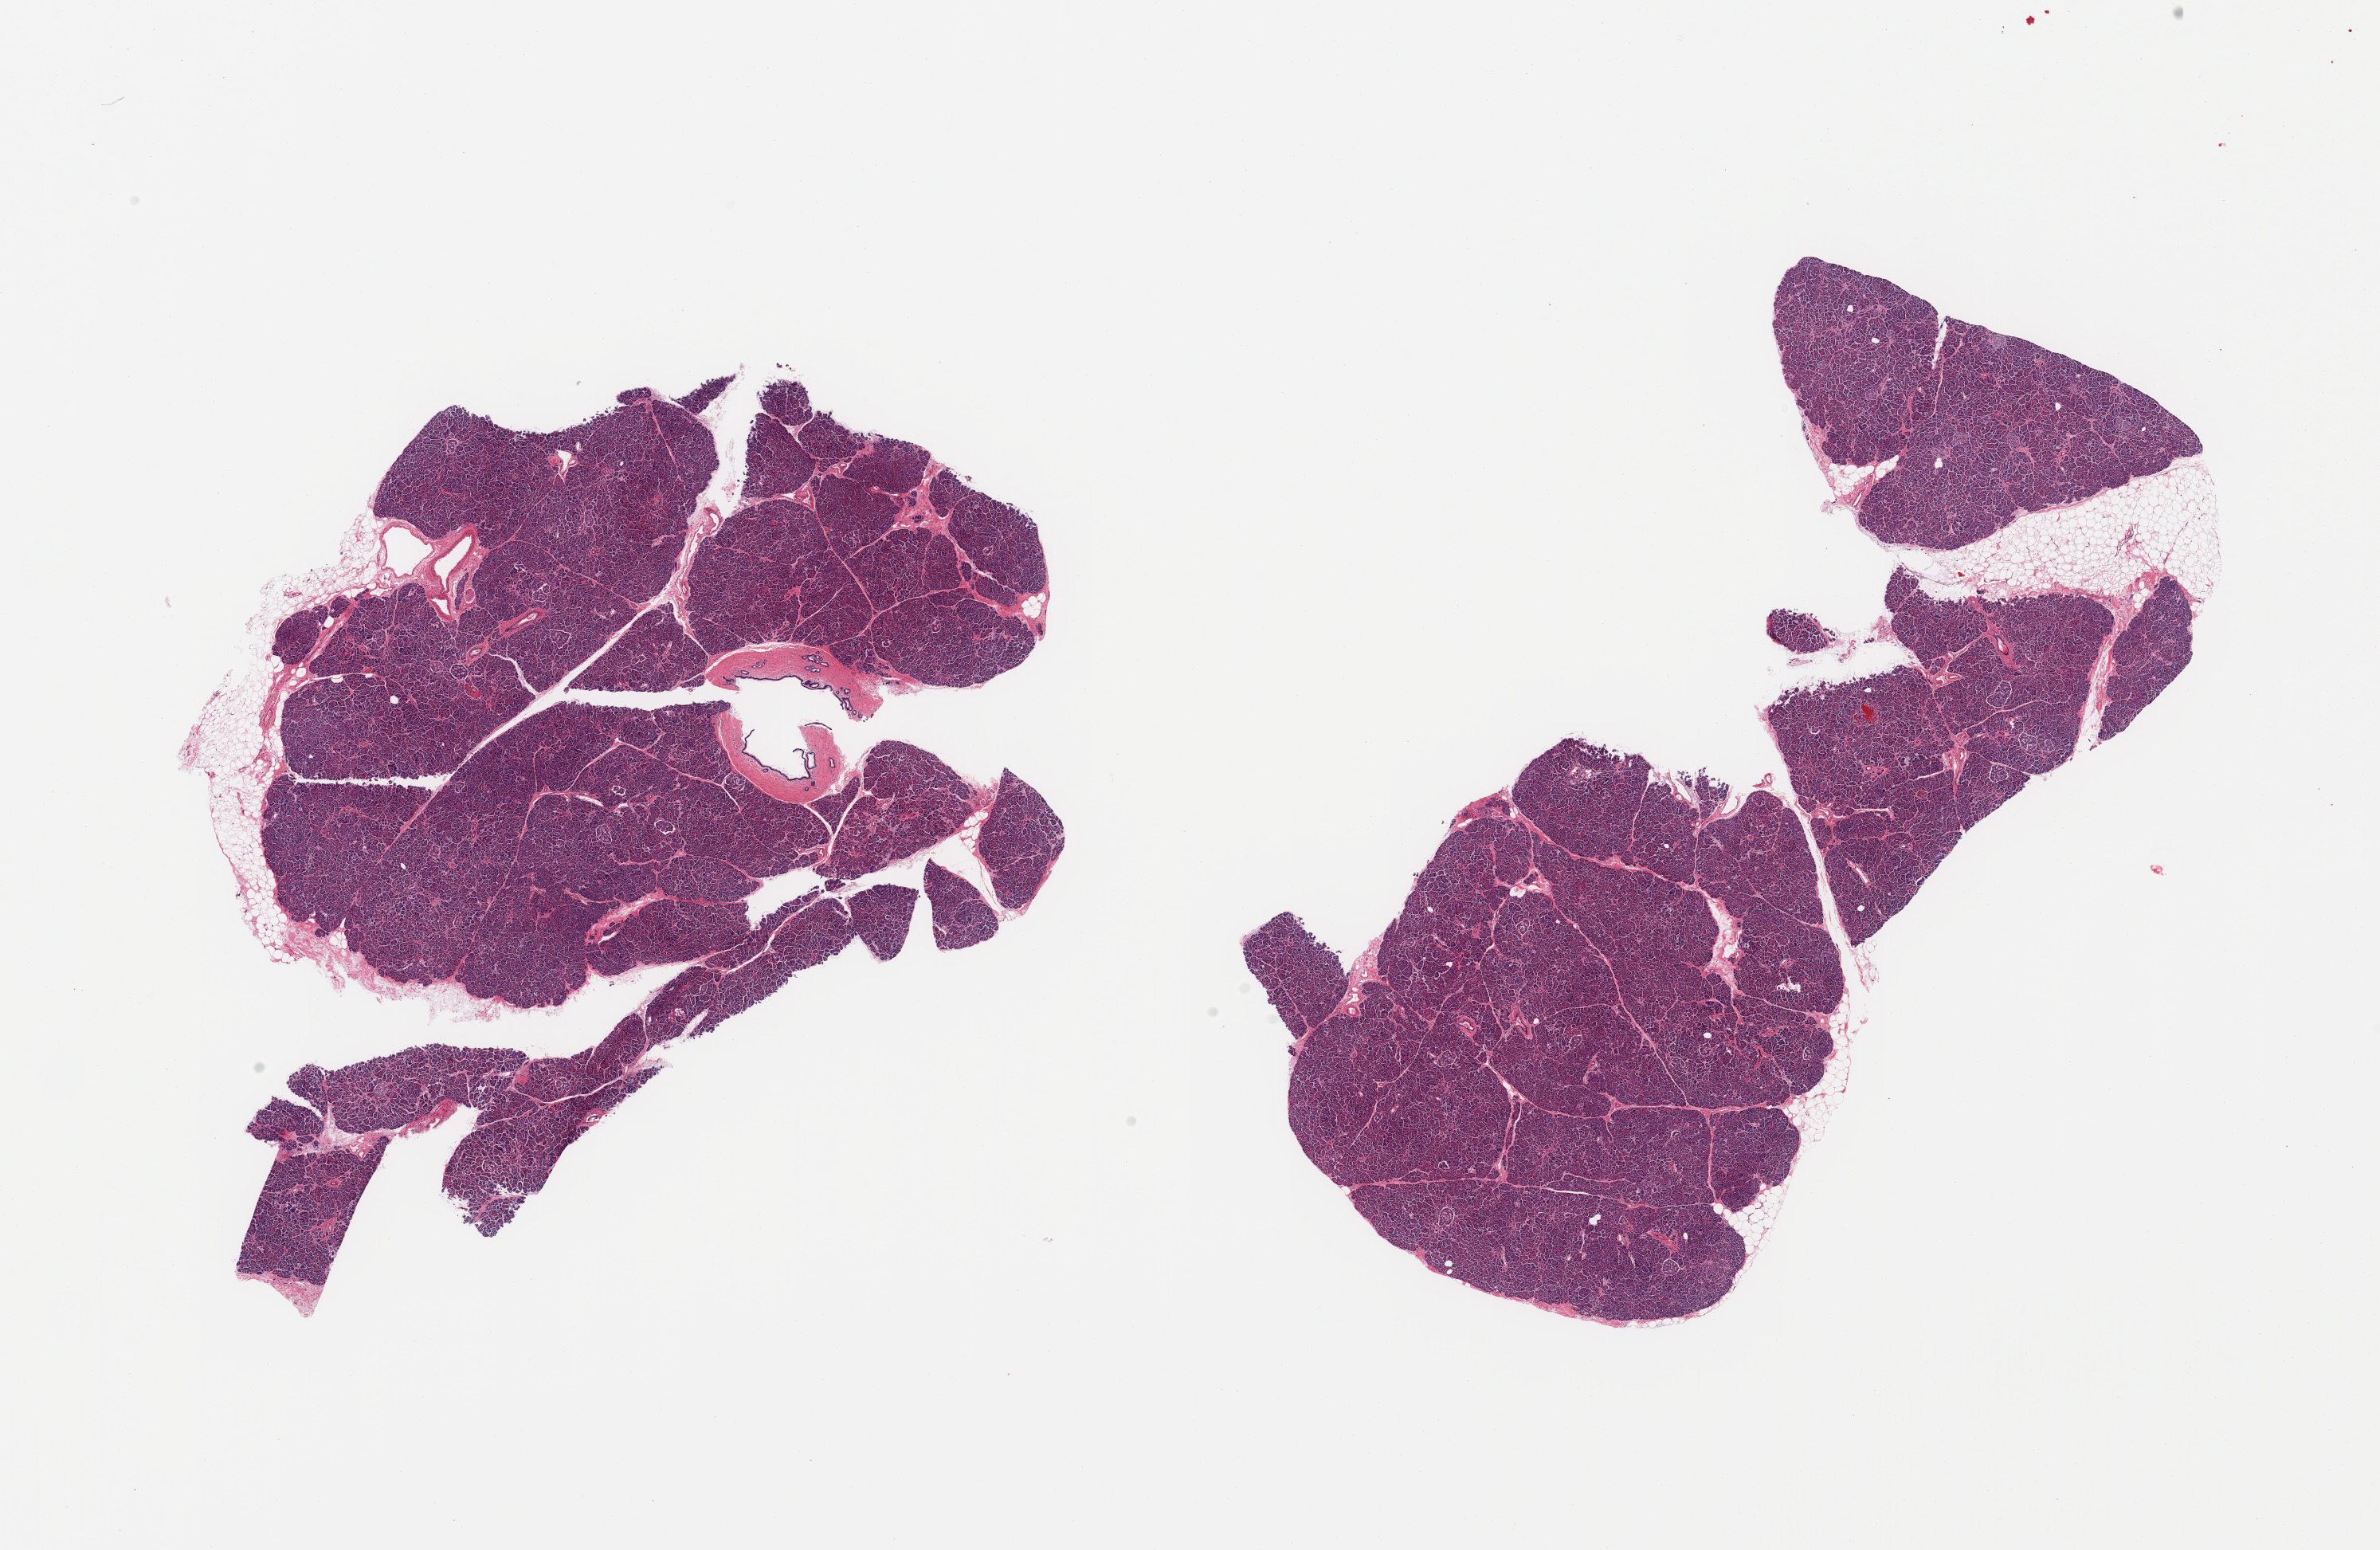
Whole-slide image, haematoxylin and eosin stain, brightfield, shown as a low-resolution overview of the whole scanned area (about 23.6 x 15.4 mm), PAXgene-fixed paraffin-embedded (PFPE) section, target tissue: pancreas, donor tissue sample. Donor sex: male.
Pathologist's review note for this sample: 2 pieces; ~5% external fat; well preserved parenchyma with Langerhans islets; mildly autolyzed fat.